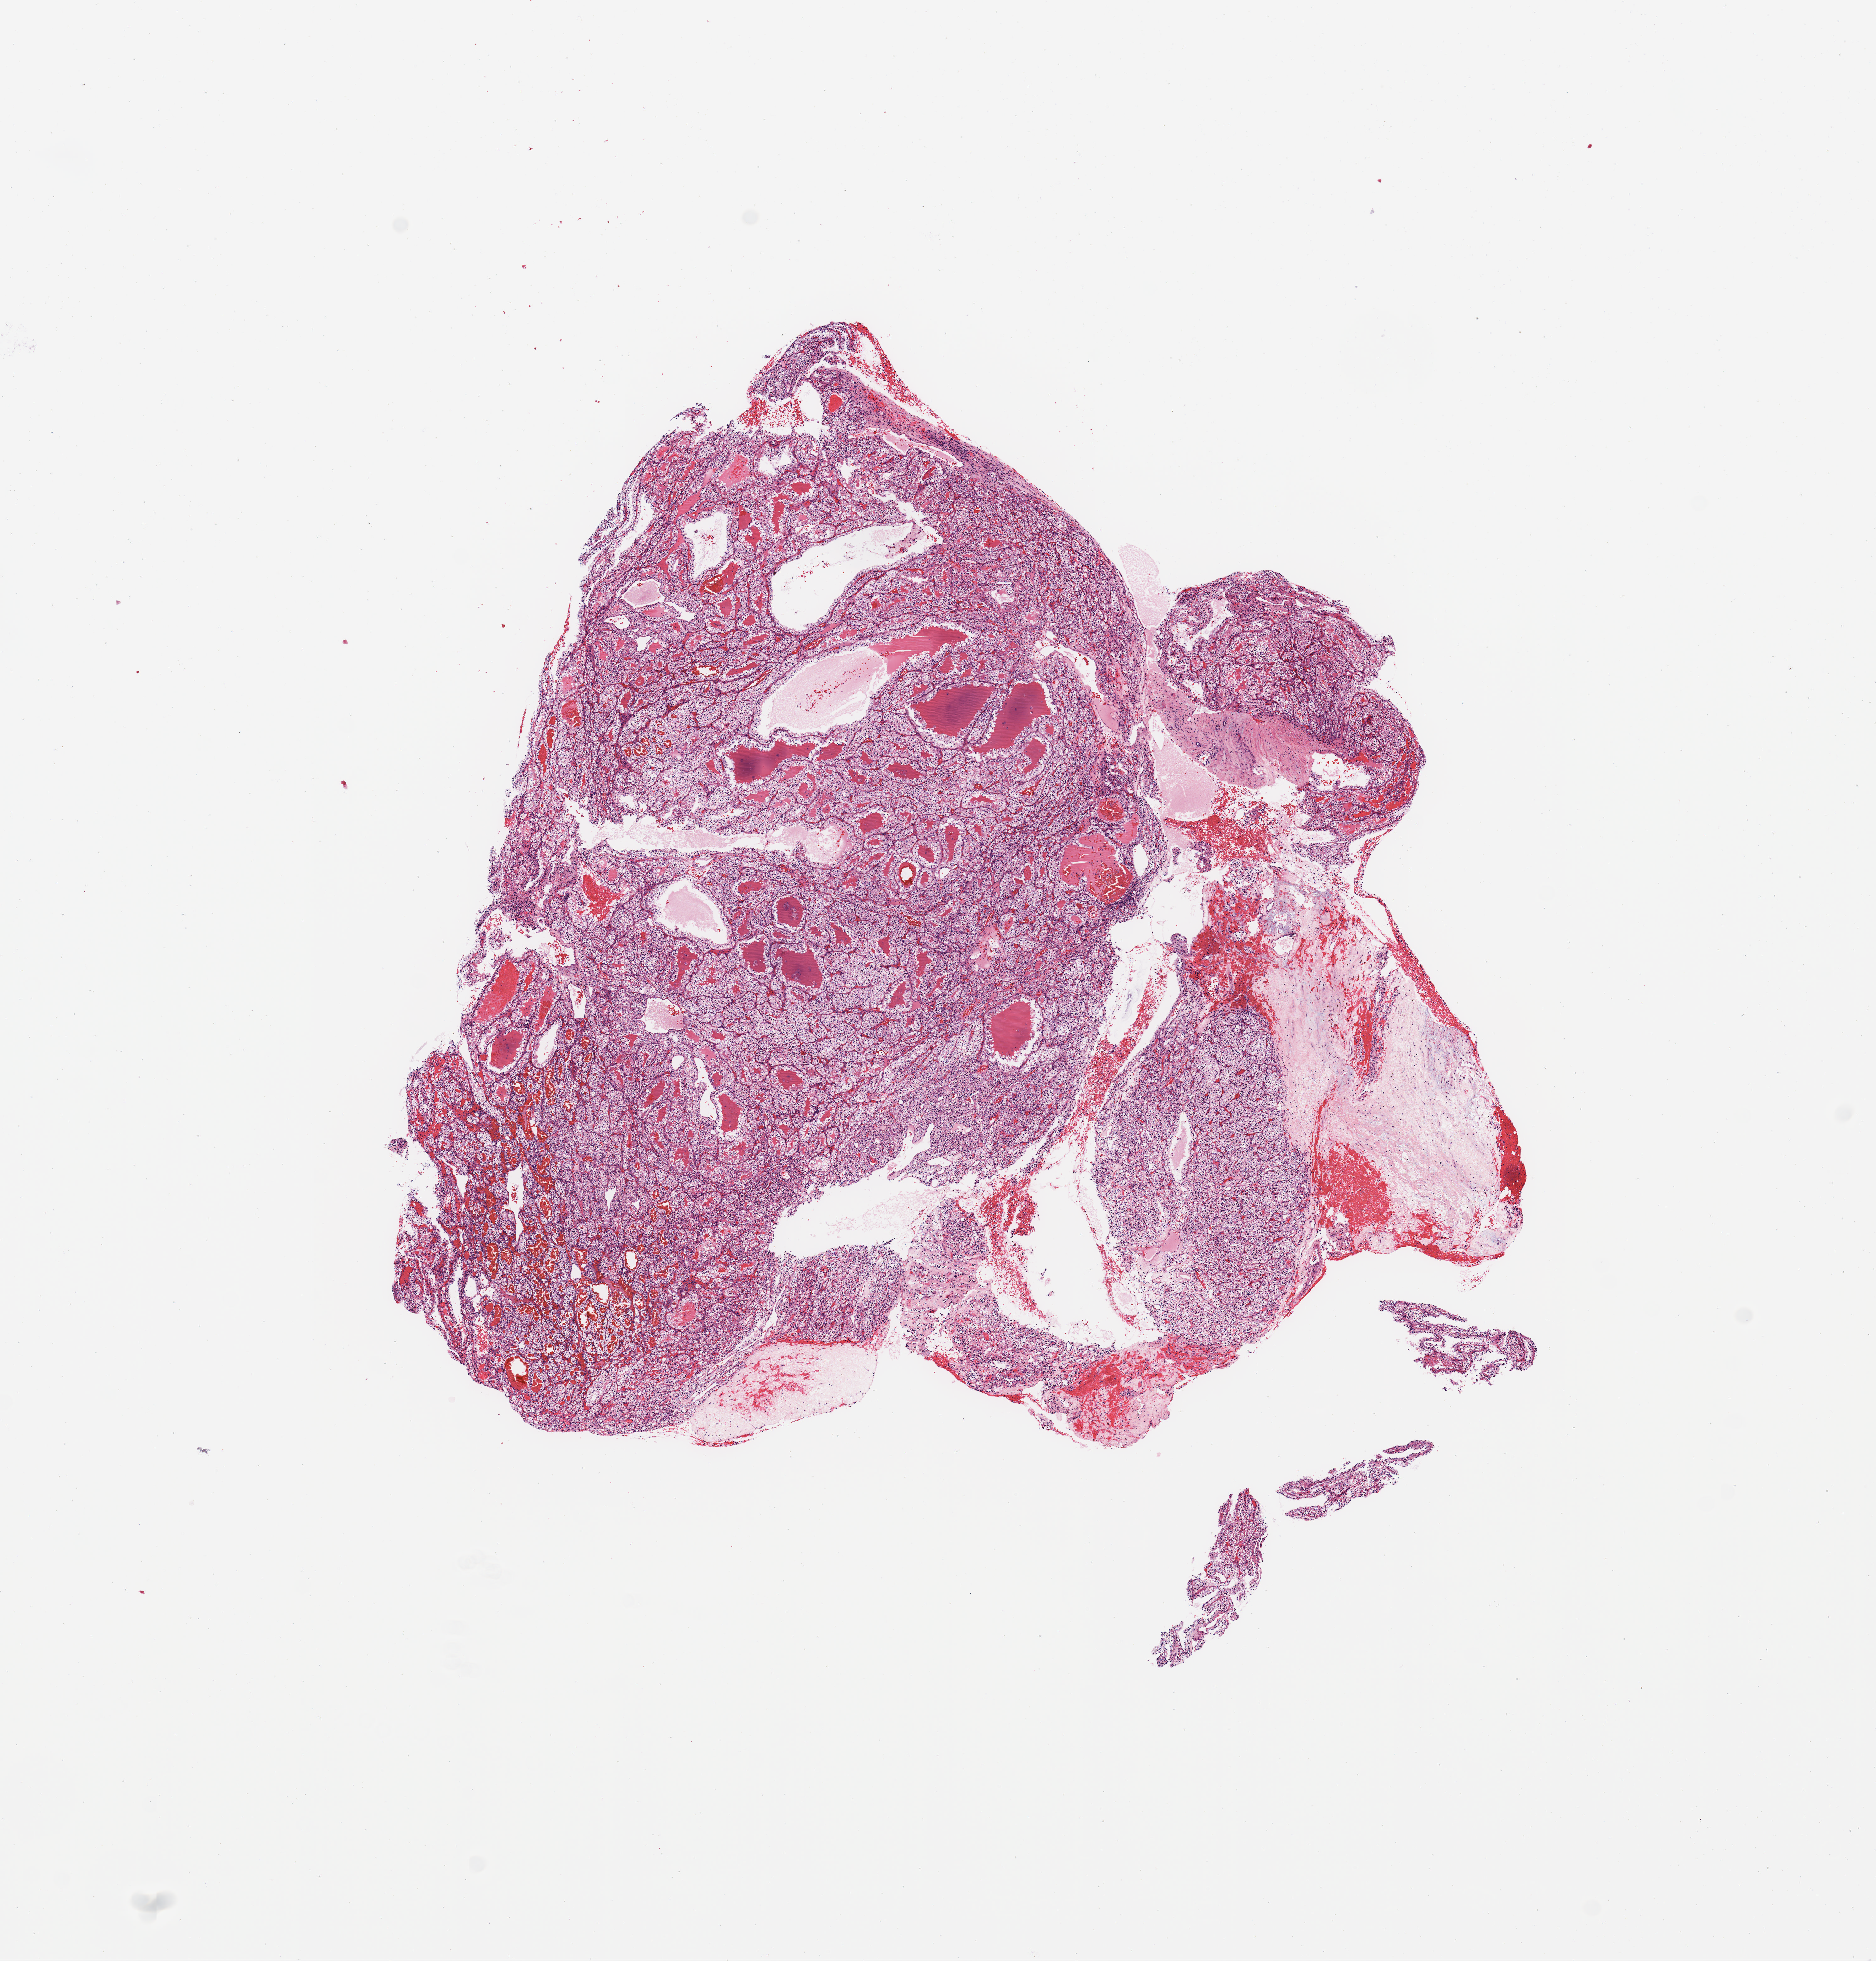
H&E whole-slide image — low-resolution overview of the scanned area, about 11.8 x 12.3 mm (slide scanned at 20x); tumour tissue sample, sampled site: kidney. 63-year-old male patient. Histologic grade: G2 (moderately differentiated). Composition of this section per pathologist review: tumour nuclei 85%, necrosis 0%.
Histologic diagnosis: Renal cell carcinoma, NOS. AJCC pathologic stage: I.